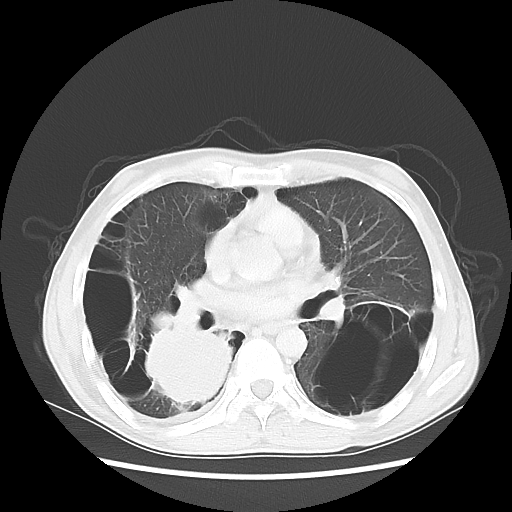
Chest CT, one axial slice; position 29 of 57 along the scan axis; 140 kVp; lung window (W 1500 / L -600 HU); 5 mm slice thickness; 512 × 512 image matrix, field of view 351 × 351 mm. Patient: male, 41 years. Case-level facts recorded for this patient, not image findings: clinical TNM (as recorded): T4 N0 M1a.
Structures marked on this image (bounding box drawn by a radiologist):
- lung tumour (recorded histology: large cell carcinoma): bounding box [x1, y1, x2, y2] px = [140, 313, 236, 412]